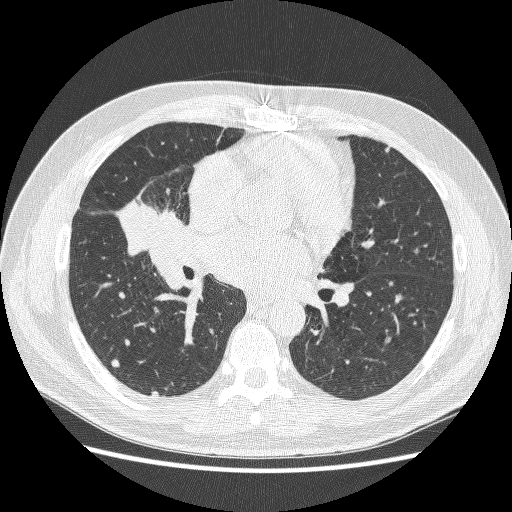
Chest CT (low-dose screening protocol), one axial image, baseline screening round, lung window (W 1500 / L -600 HU), 1.25 mm slice thickness, lung (sharp) reconstruction kernel (BONE), slice 136 of 251 in the series, 512 × 512 image matrix, field of view 360 × 360 mm. Male participant, aged 59 years at enrolment. Former smoker at enrolment.
Expert reader's lesion annotation, bounding box (x1, y1, x2, y2) in pixels: (120, 184, 197, 259). No non-calcified nodule or mass ≥4 mm was recorded by the screening reader at this exam. Later outcome: lung cancer diagnosed 24 days after this screen — adenocarcinoma, NOS, right middle lobe, poorly differentiated (G3), stage IV (AJCC 6th edition), 54 mm at pathology.